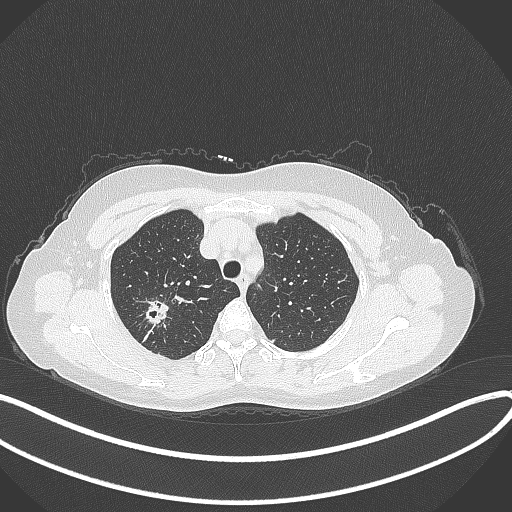
Chest CT, one axial slice. Slice 291 of 337 in the series (ordered by position). Reconstruction kernel B70f. 120 kVp. Lung window (W 1500 / L -600 HU). 1 mm slice thickness. 512 × 512 image matrix, field of view 400 × 400 mm. Patient: female, 50 years. From the clinical record (not read from this slice): clinical TNM (as recorded): T1c N0 M0.
Structures marked on this image (rectangle marked by the reading radiologist):
- lung tumour (recorded histology: adenocarcinoma): bounding box [x1, y1, x2, y2] px = [137, 294, 173, 328]